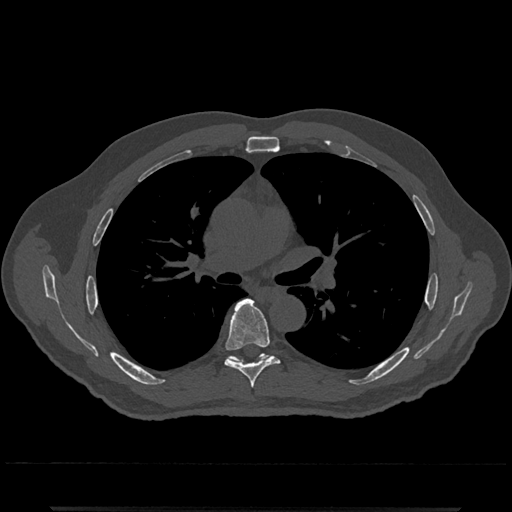
CT including the spine, one axial slice. Slice 767 of 797 in the series (ordered by position). 120 kVp. Bone window (W 1800 / L 400 HU). 512 × 512 image matrix. Patient: male, 67 years. Case-level facts recorded for this patient, not image findings: primary cancer: prostate.
Outlined on this slice (semi-automatic segmentation, software-assisted and operator-edited):
- T6 vertebra: box from (x=223, y=299) to (x=279, y=388) px
- T7 vertebra: (x=228, y=354)–(x=269, y=363)